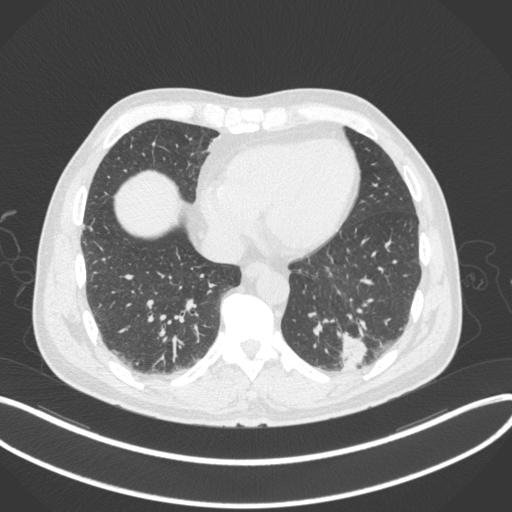
Chest CT, one axial slice; position 85 of 313 along the scan axis; reconstruction kernel B31f; lung window (W 1500 / L -600 HU); 1 mm slice thickness; 512 × 512 image matrix, field of view 400 × 400 mm. Patient: male, 54 years. From the clinical record (not read from this slice): clinical TNM (as recorded): T1c N0 M1; histopathological grade: G3.
Annotated regions visible in this slice (rectangle marked by the reading radiologist):
- lung tumour (recorded histology: adenocarcinoma): bounding box <329,325,370,375> (left, top, right, bottom; pixels)